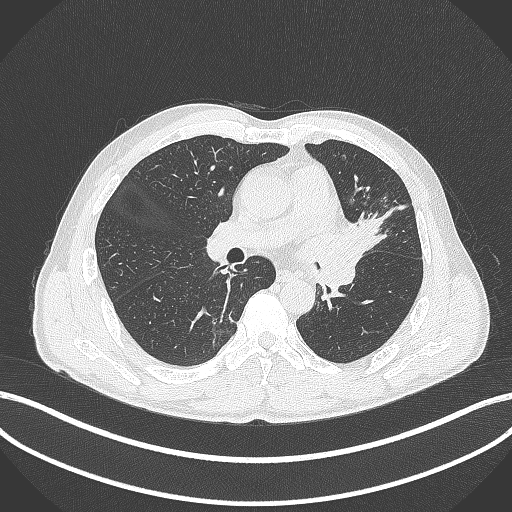
Chest CT, one axial slice; slice 233 of 429 in the series (ordered by position); reconstruction kernel B70f; 120 kVp; lung window (W 1500 / L -600 HU); 512 × 512 image matrix, field of view 400 × 400 mm. Male patient, age 57 years. From the clinical record (not read from this slice): clinical TNM (as recorded): T2b N0 M0.
Outlined on this slice (bounding box drawn by a radiologist):
- lung tumour (recorded histology: squamous cell carcinoma): bounding box (x1, y1, x2, y2) in pixels: (326, 204, 379, 269)